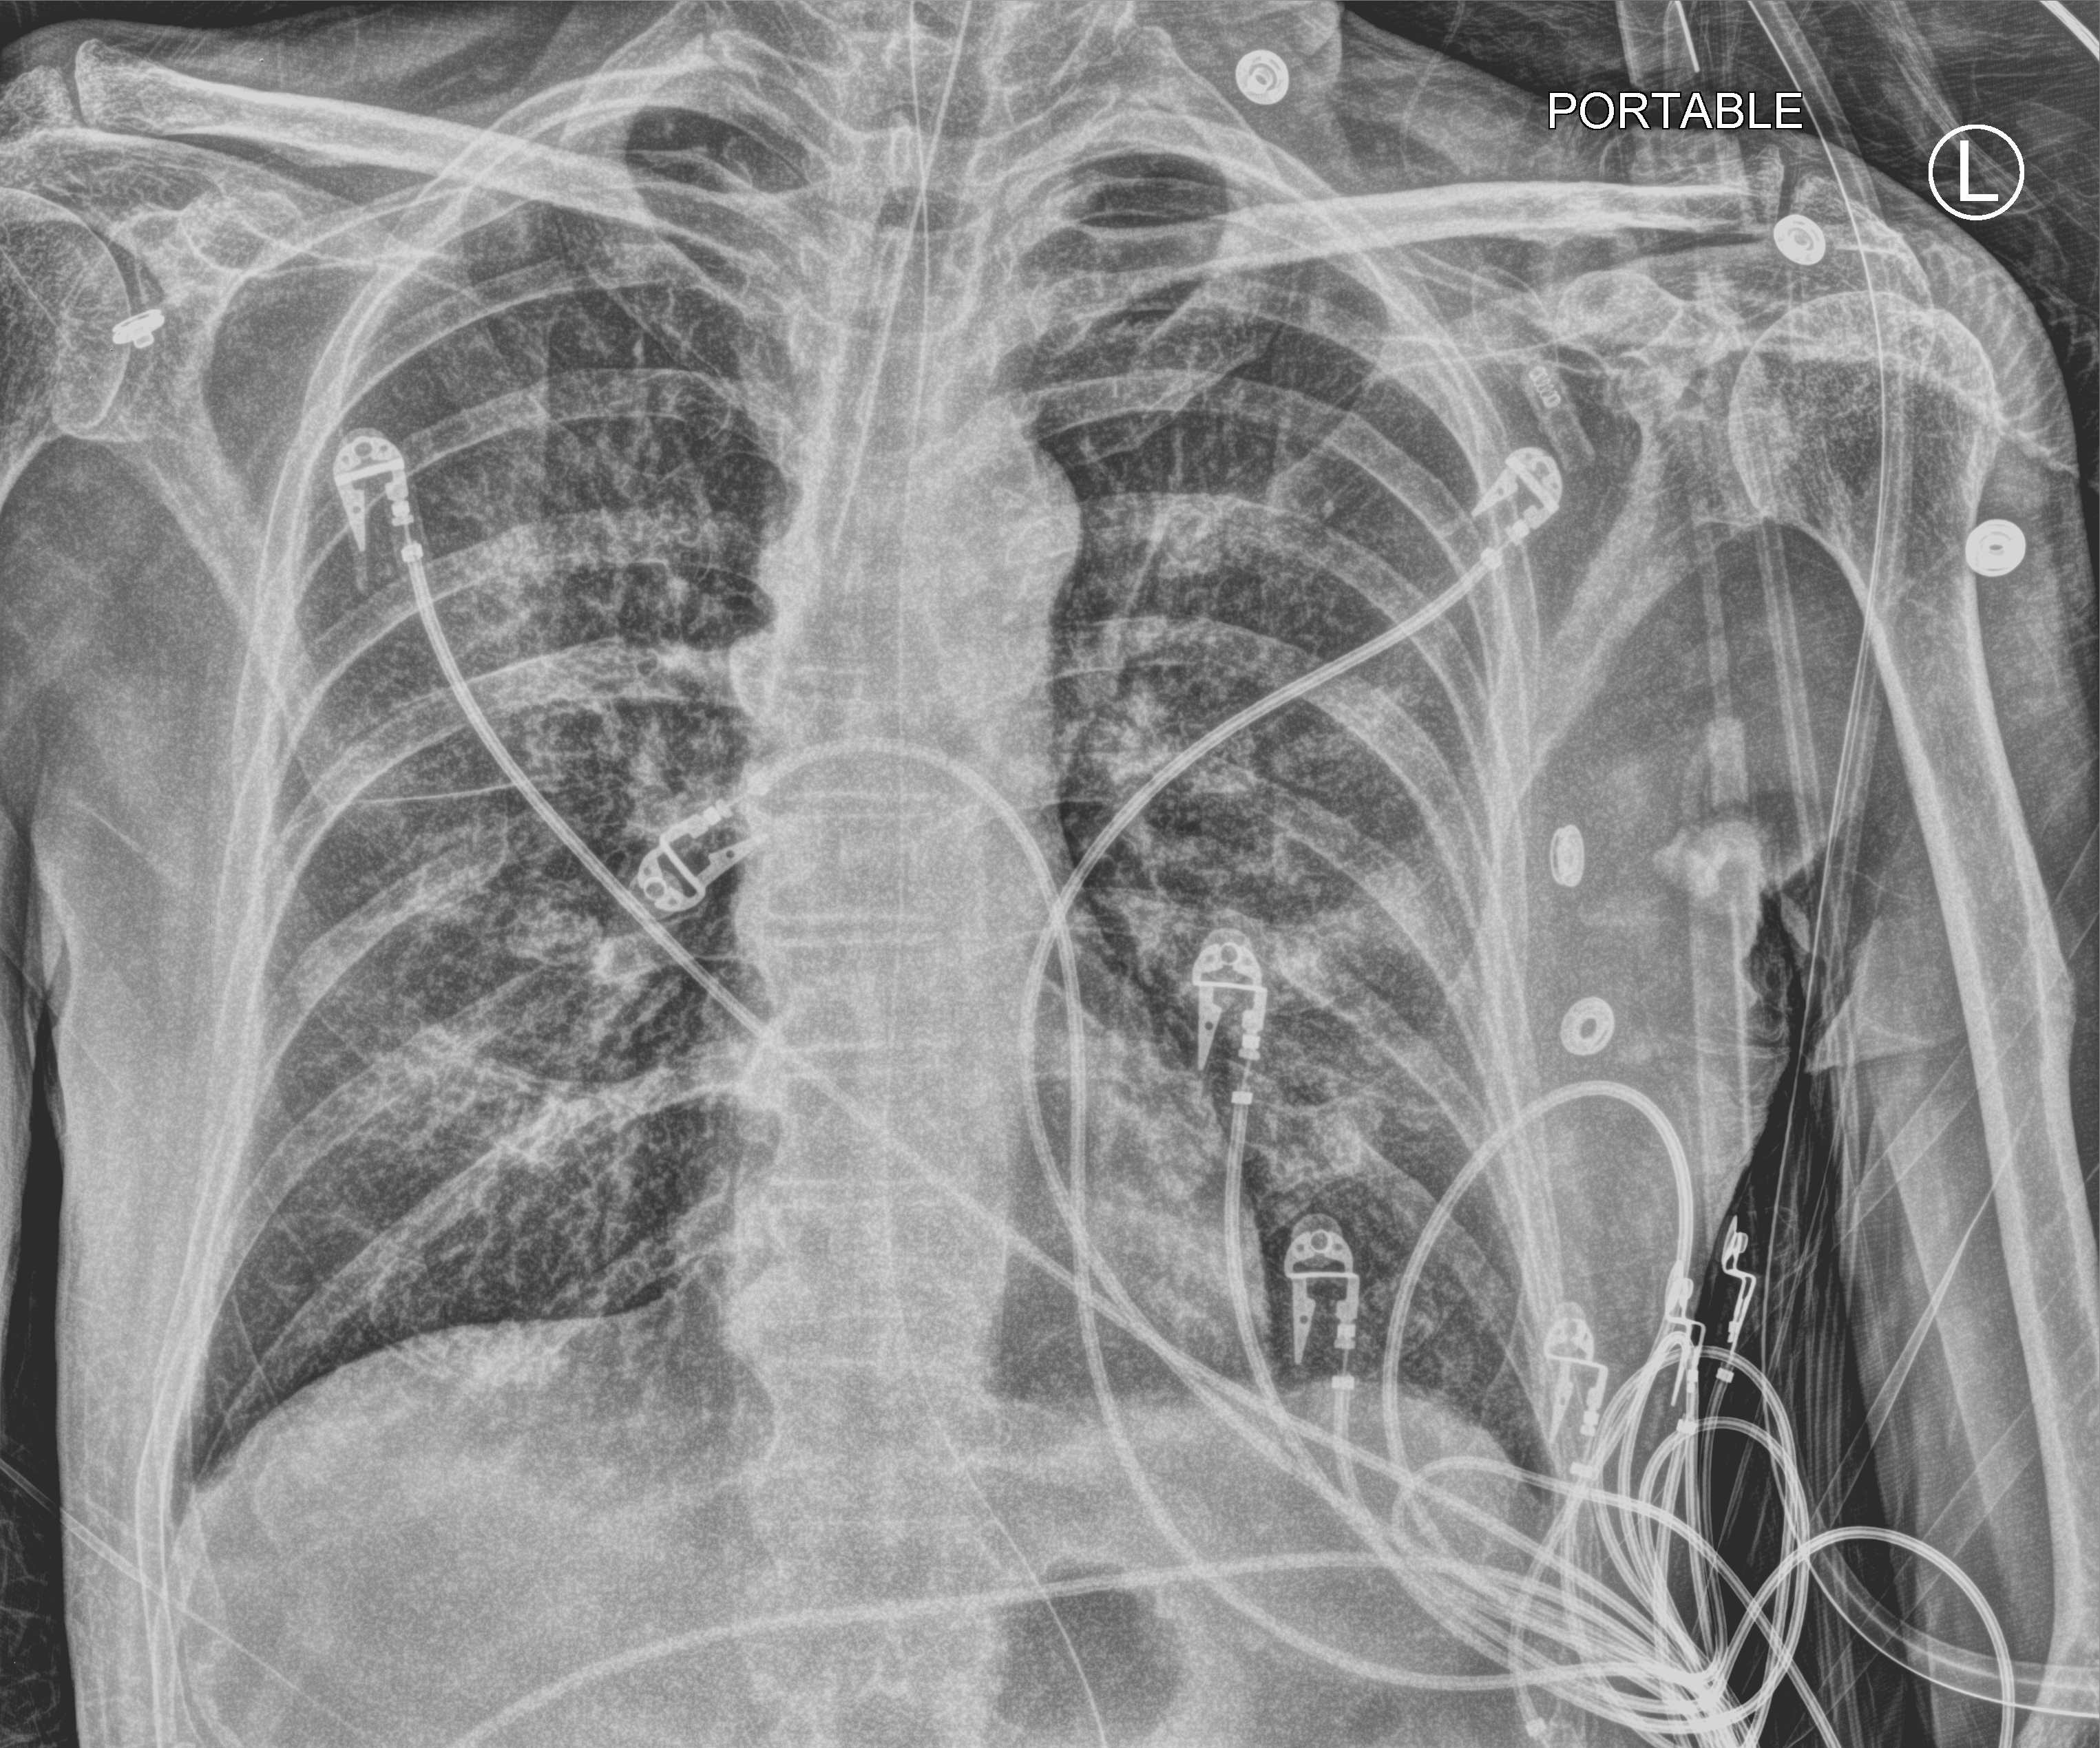
Chest X-ray (portable), anteroposterior (AP) projection. Patient hospitalised with COVID-19; male, aged 60–74 years.
From the hospital-stay record, not from the radiograph (when in the stay this image was taken is not recorded): length of hospital stay: 42 days.